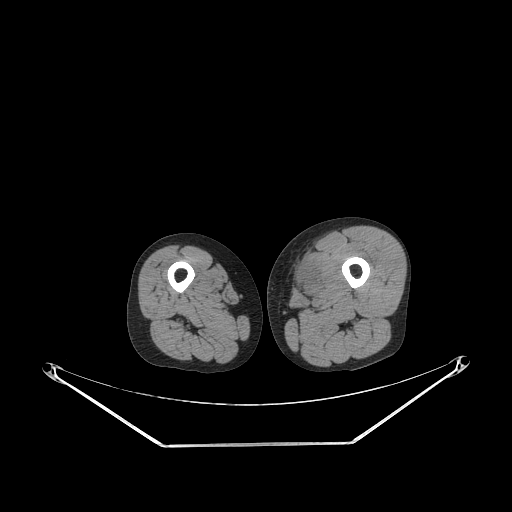
CT of an extremity soft-tissue mass (from a PET/CT study), one axial slice. Position 227 of 267 along the scan axis. 140 kVp. Soft-tissue window (W 400 / L 40 HU). 3.75 mm slice thickness. 512 × 512 image matrix, field of view 500 × 500 mm. Male patient. Case-level facts recorded for this patient, not image findings: histological type: pleiomorphic leiomyosarcoma; grade: high; site of the primary tumour: left thigh.
Structures marked on this image (expert contour drawn on MRI and transferred to this co-registered scan by the dataset authors):
- gross tumour volume including surrounding oedema: box from (x=290, y=254) to (x=323, y=293) px
- gross tumour volume (mass): (x=292, y=260)–(x=316, y=291)